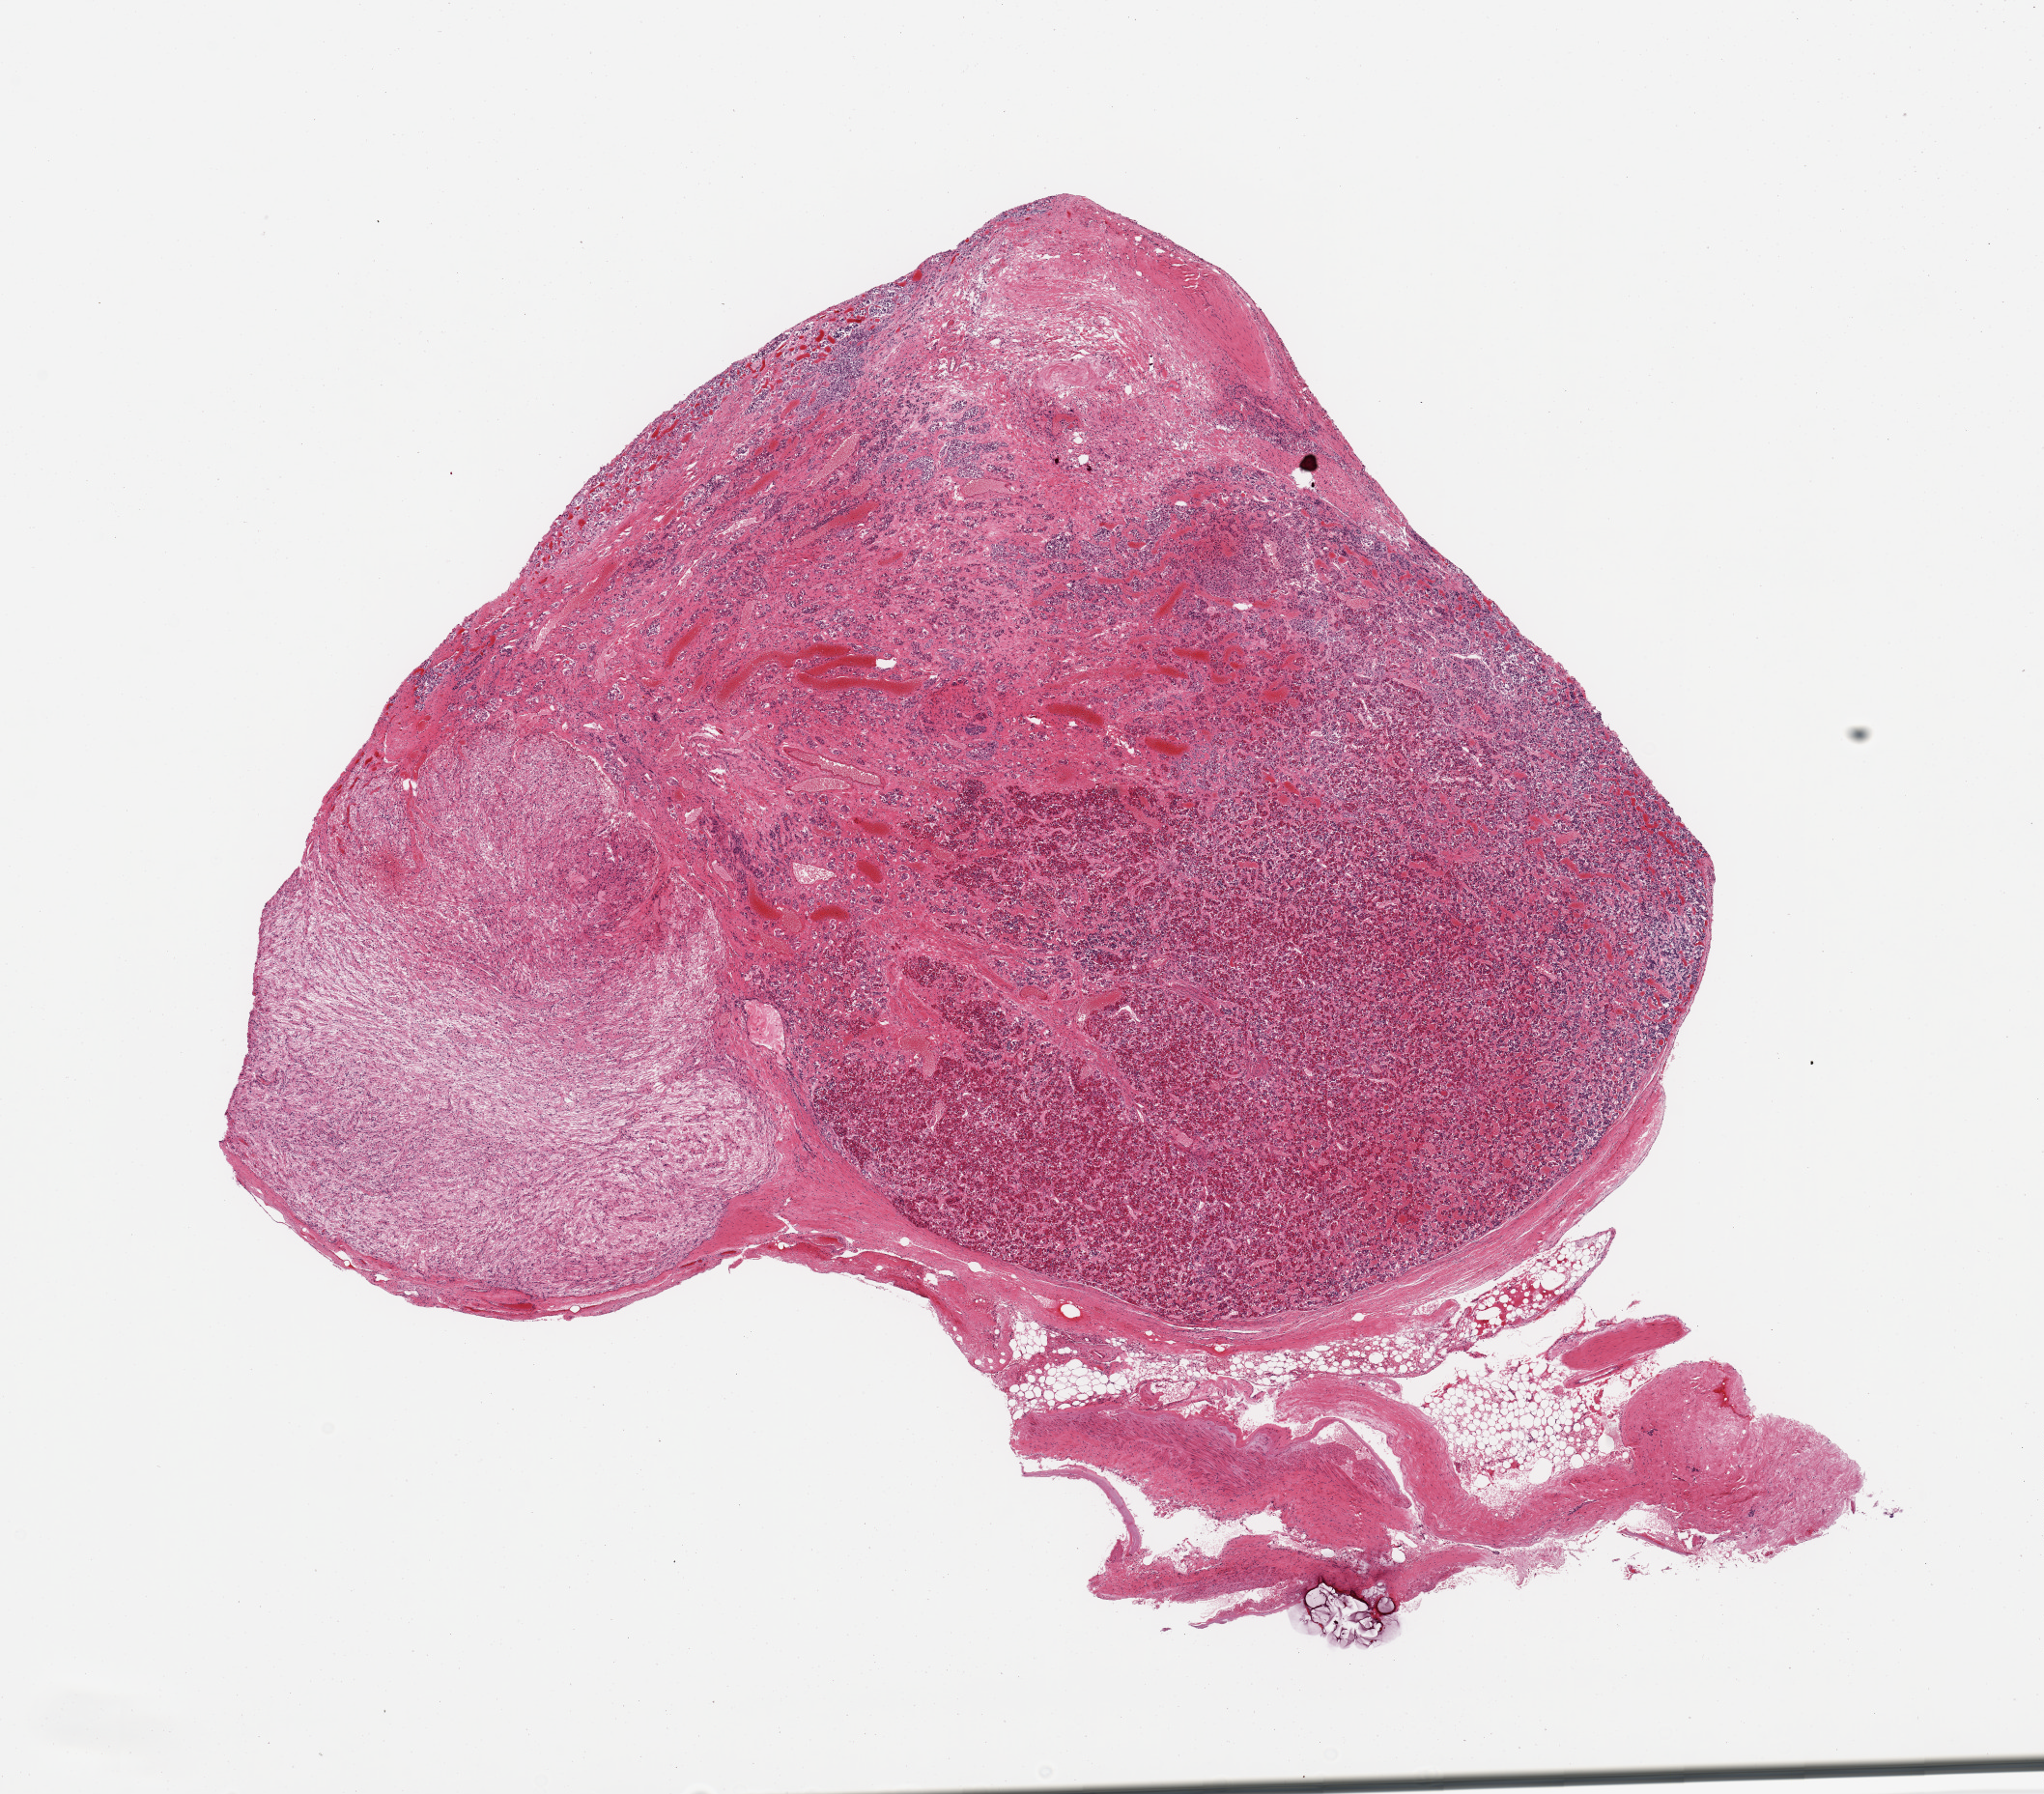
Haematoxylin and eosin whole-slide image, low-resolution overview of the scanned area, about 16.7 x 14.7 mm (from a 20x scan). PAXgene-fixed paraffin-embedded (PFPE) section. Sampled site (target tissue): pituitary. Tissue donor sample. Female donor.
* pathologist's review note for this sample: 1 piece; mainly adenophypophysis; ~4.5mm foculs of neurohypophysis; ~7mm nubbin of adherent dura